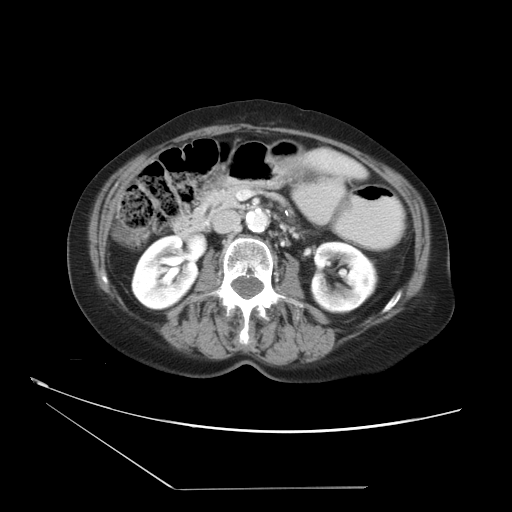
Contrast-enhanced abdominal CT, one axial slice; slice 11 of 36 in the series (ordered by position); intravenous contrast given; soft-tissue window (W 400 / L 40 HU); 5 mm slice thickness; 512 × 512 image matrix. Female patient, age 81 years. Case-level facts recorded for this patient, not image findings: diagnosis: colorectal cancer liver metastases, imaged before liver resection; multiple liver metastases: no; largest metastasis: 1.6 cm.
Structures marked on this image (manually delineated by an expert):
- liver: bounding box [x1, y1, x2, y2] px = [300, 150, 364, 179]